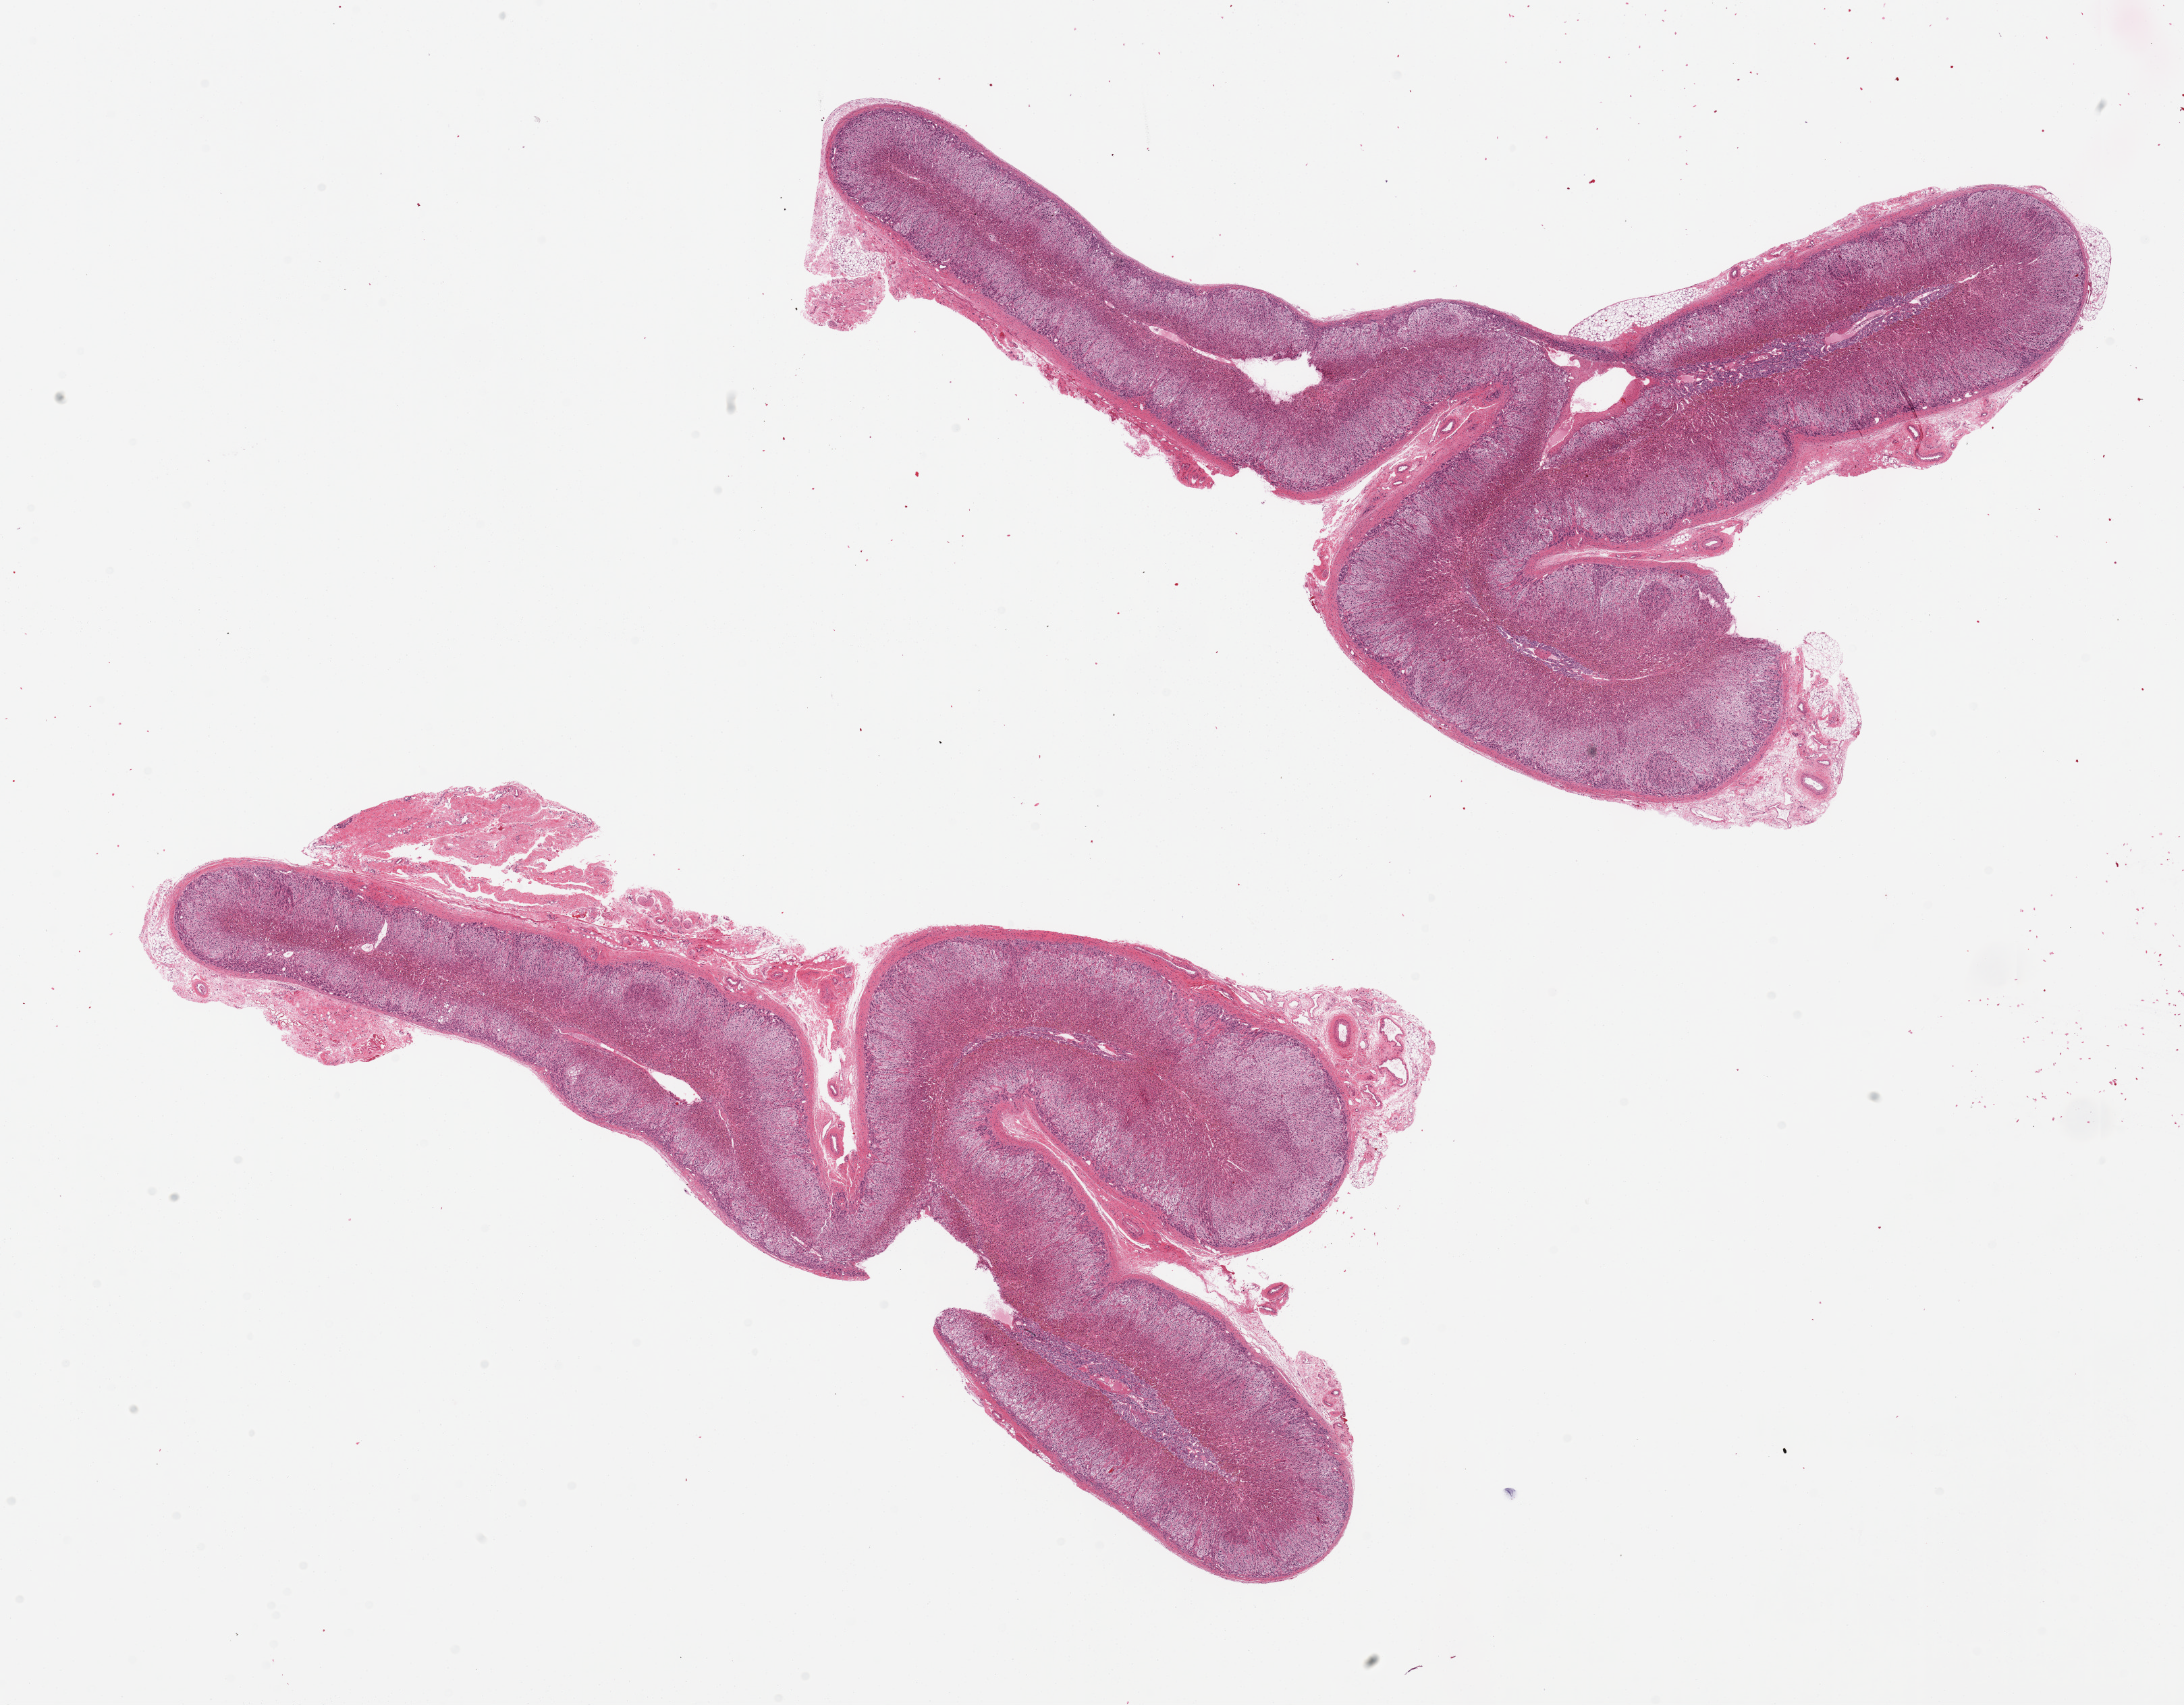
Haematoxylin and eosin whole-slide image, brightfield — low-resolution overview of the scanned area, about 25.6 x 20.0 mm. PAXgene-fixed paraffin-embedded (PFPE) section. Sampled site (target tissue): adrenal gland. Donor tissue sample. Male donor.
Reviewer comment on this tissue sample: 2 pieces; well trimmed except for 10-20% external stroma.